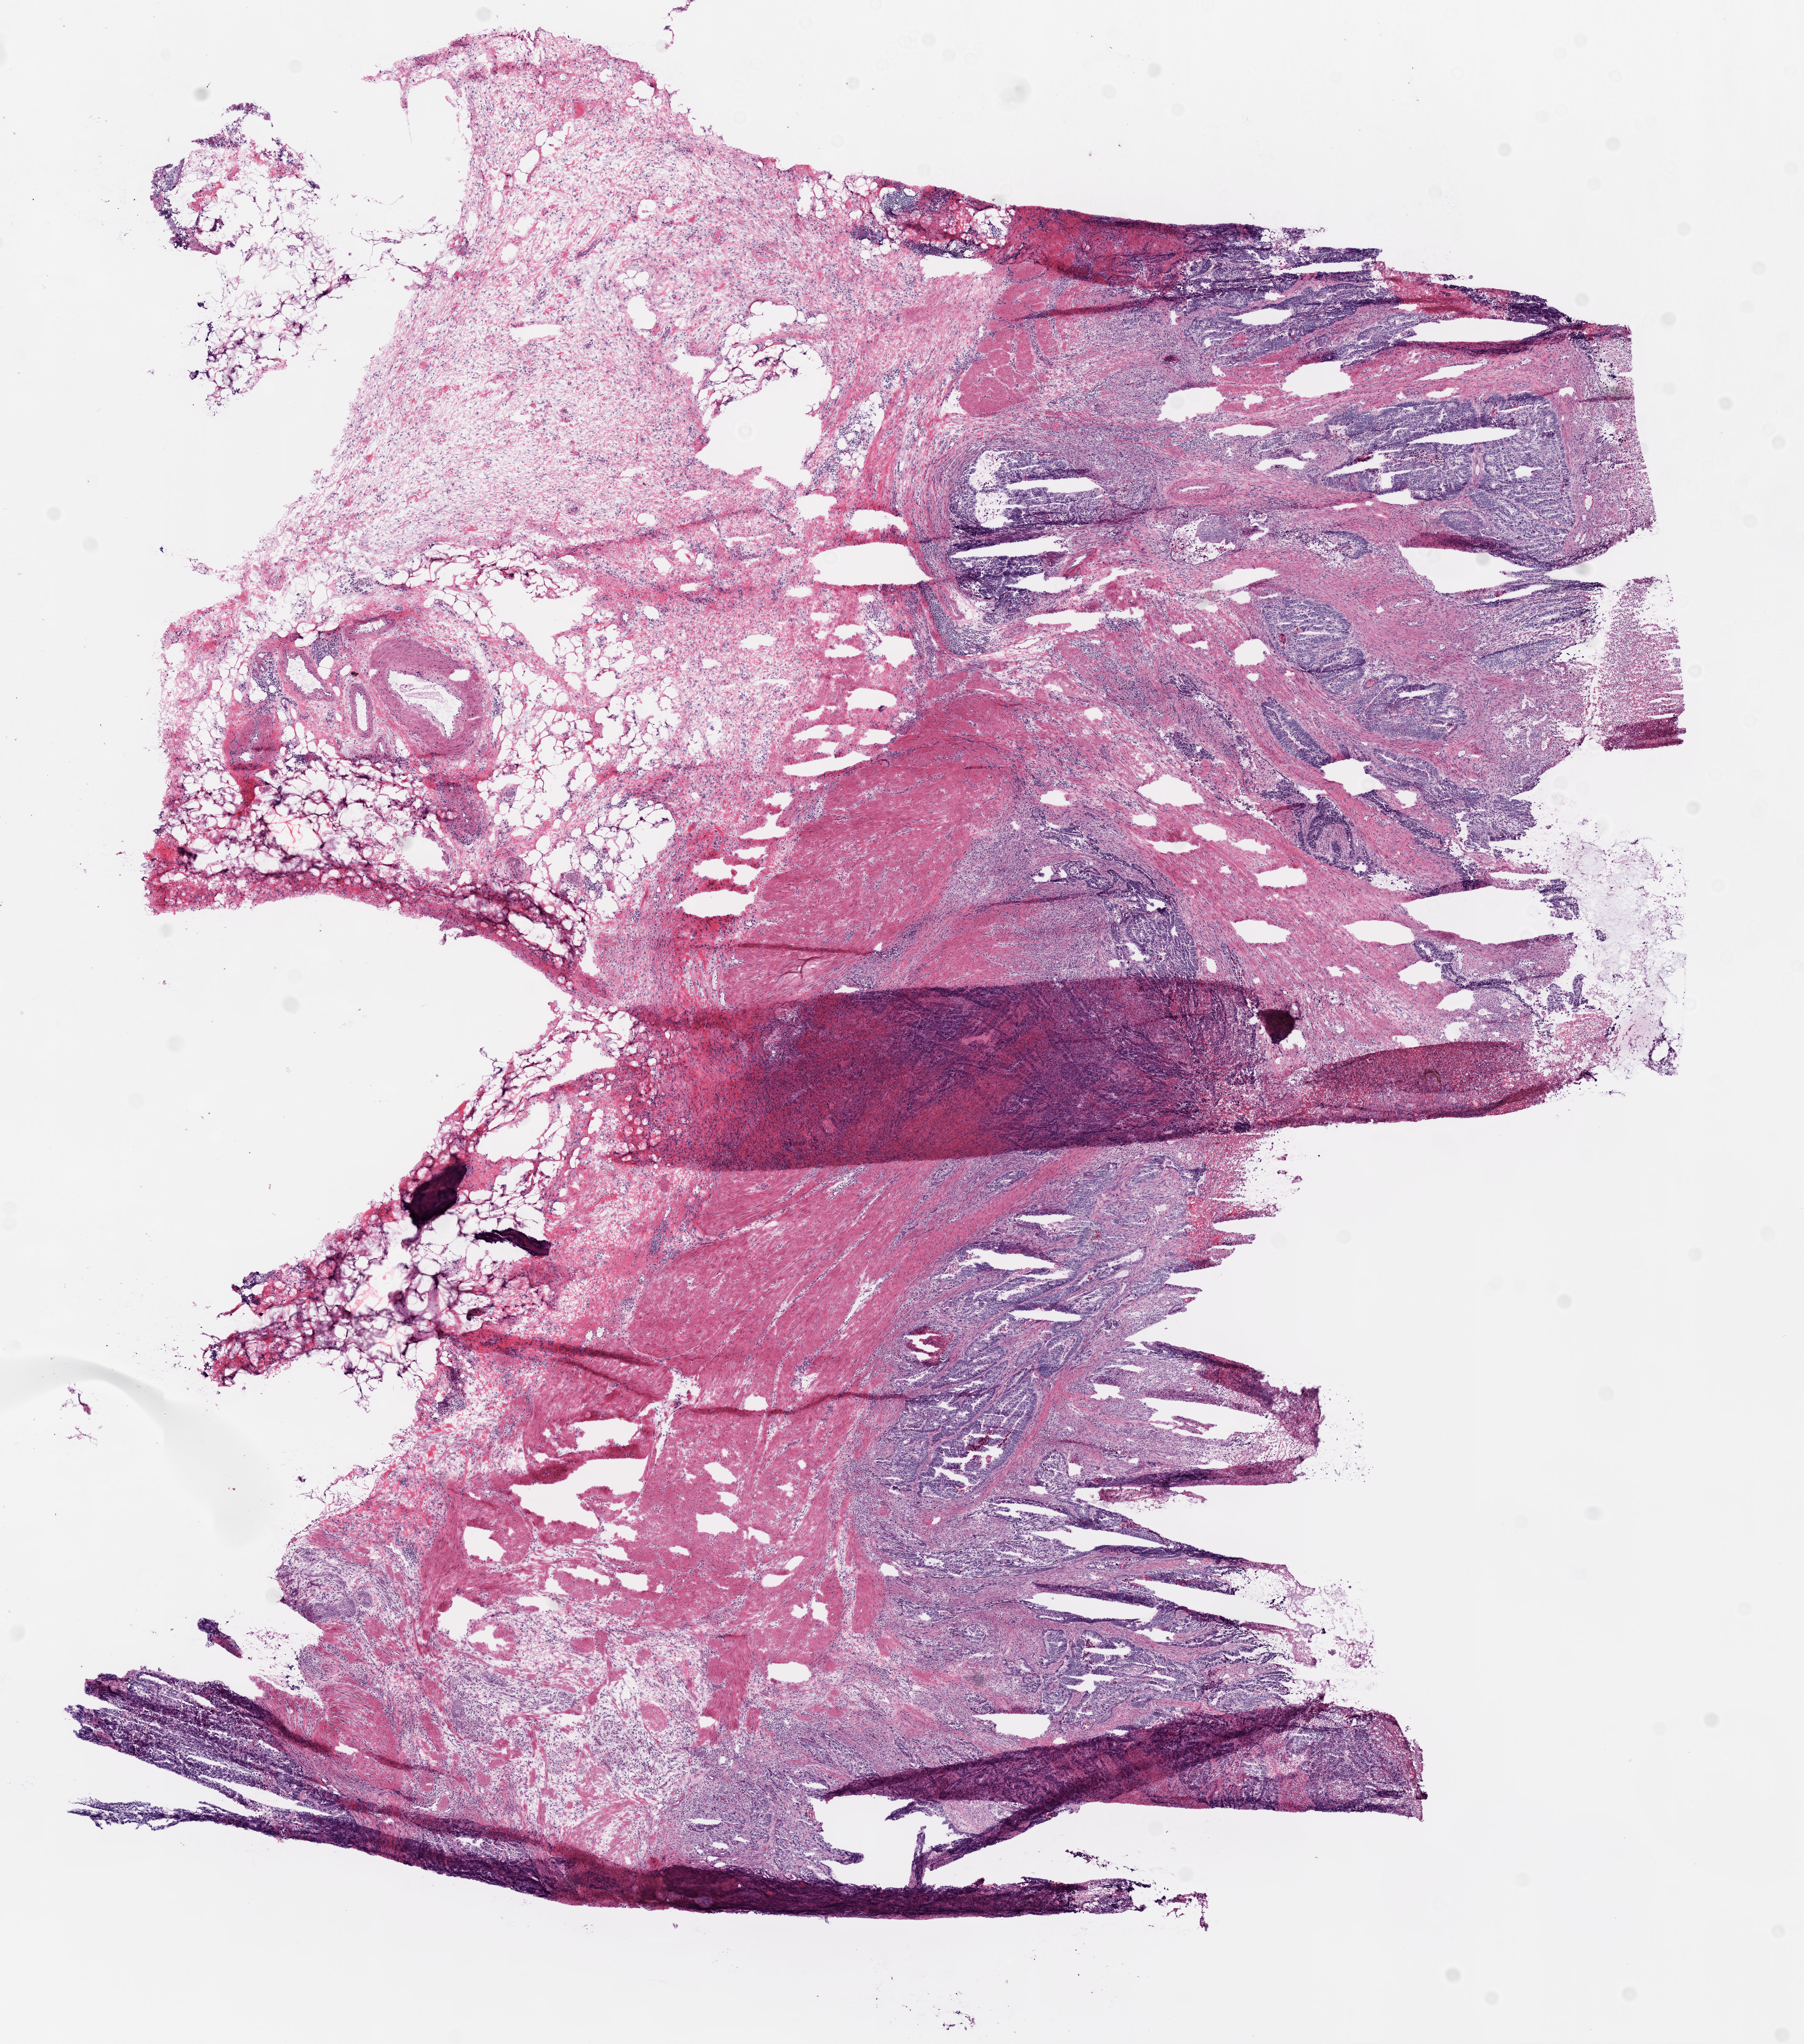
Digitized Hematoxylin and eosin (H&E) stained tissue section (whole slide) — low-resolution overview of the scanned area, about 11.0 x 12.5 mm (from a 20x scan); frozen section from the bottom of the tissue portion; primary tumour sample from the rectum. Male patient; age at initial diagnosis 57 years. Composition of this section per pathologist review: tumour cells 42%, tumour nuclei 70%, normal cells 50%, stromal cells 5%, necrosis 3%.
- pathologic diagnosis: Adenocarcinoma, NOS (rectosigmoid junction)
- TNM: T3 N2 M0
- AJCC pathologic stage: IIIC